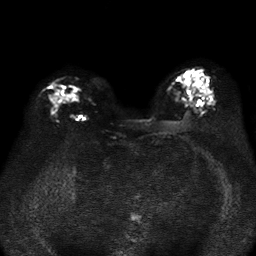
Breast MRI, one axial slice; diffusion-weighted series; image 2 of 4 stored at this slice position (different b-values; order by instance number); 1.5 T; 256 × 256 image matrix, field of view 320 × 320 mm. Female patient.
Outlined on this slice (manually delineated by an expert):
- tumour on diffusion-weighted imaging: bounding box <52,89,73,101> (left, top, right, bottom; pixels)